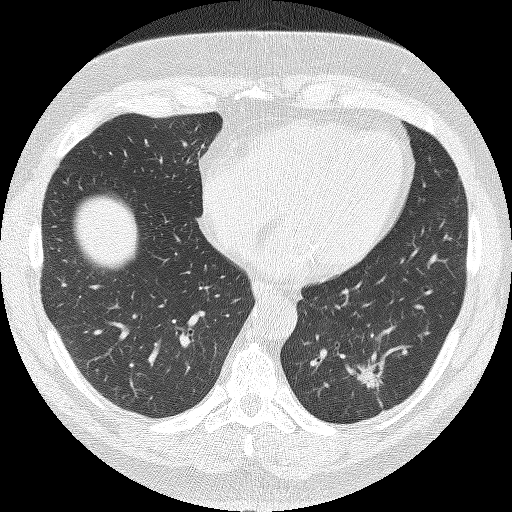
Low-dose screening chest CT, one axial slice. Position 46 of 140 along the scan axis. Reconstruction kernel FC51. 120 kVp. Lung window (W 1500 / L -600 HU). 2 mm slice thickness. 512 × 512 image matrix, field of view 349 × 349 mm.
Structures marked on this image (outlined manually by an expert reader):
- lesion 1 (tumor, lower lobe of left lung): box from (x=357, y=362) to (x=384, y=391) px